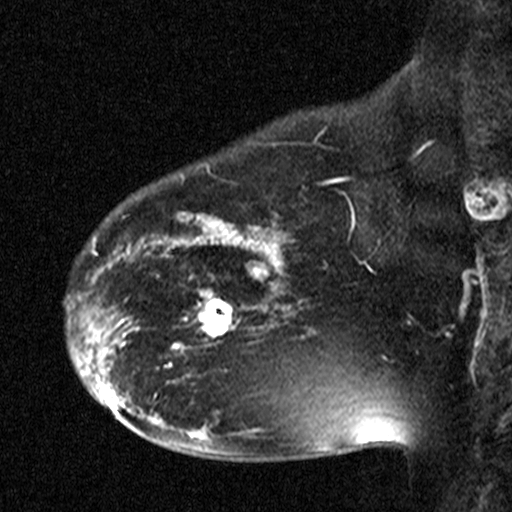
Breast MRI (dynamic contrast-enhanced), one sagittal slice. Position 32 of 44 along the scan axis. Dynamic contrast-enhanced study with each time point stored as its own series, time point 2 of 3 at this slice position (early post-contrast, ordered by acquisition time). 1.5 T. TE 4.5 ms, TR 11 ms. 512 × 512 image matrix, field of view 200 × 200 mm. Female patient, age 38 years. From the clinical record (not read from this slice): setting: breast cancer imaged before/during neoadjuvant chemotherapy; receptor status: HR-positive, HER2-negative.
Annotated regions visible in this slice (semi-automatic segmentation, software-assisted and operator-edited):
- analysis volume of interest (the breast-tissue region the enhancement analysis was run in; not a lesion): bounding box (x1, y1, x2, y2) in pixels: (176, 272, 251, 349)
- tumour enhancement mask (voxels above the 90 % enhancement threshold inside the analysis volume of interest): (176, 275, 244, 348)